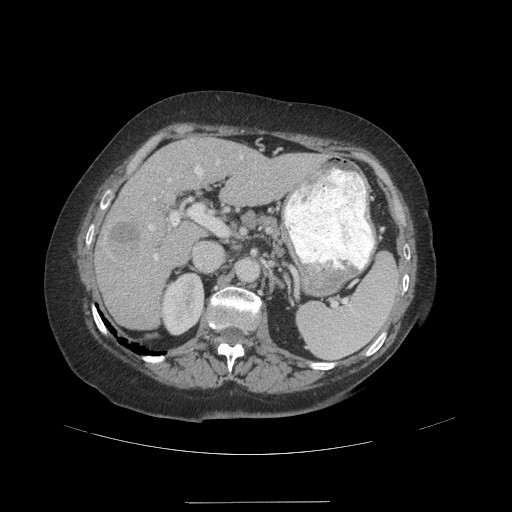
Contrast-enhanced abdominal CT (liver protocol), one axial slice. Slice 62 of 99 in the series (ordered by position). Reconstruction kernel STANDARD. Soft-tissue window (W 400 / L 40 HU). 2.5 mm slice thickness. 512 × 512 image matrix, field of view 440 × 440 mm. Case-level facts recorded for this patient, not image findings: diagnosis: hepatocellular carcinoma (patient treated with transarterial chemoembolisation; whether this scan precedes or follows treatment is not stated here); TNM stage (as recorded): Stage-IVA; Child-Pugh class: A.
Annotated regions visible in this slice (semi-automatic segmentation, software-assisted and operator-edited):
- liver parenchyma outside the tumour (the mass and vessels are separate outlines, so this box may not span the whole liver): bounding box [x1, y1, x2, y2] px = [94, 136, 323, 330]
- mass: [107, 222, 139, 259]
- liver vessels: [148, 155, 243, 261]